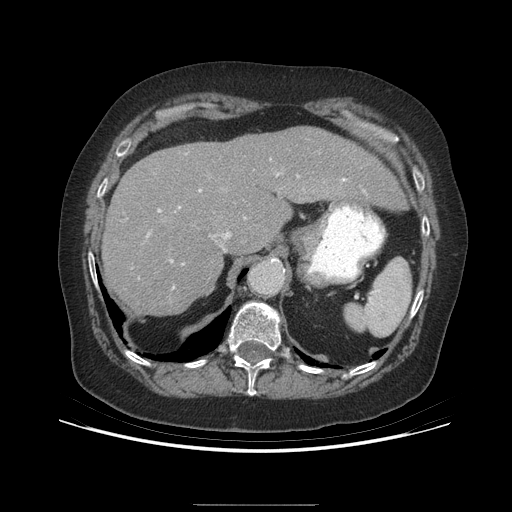
Contrast-enhanced abdominal CT (liver protocol), one axial slice. Reconstruction kernel STANDARD. 140 kVp. Soft-tissue window (W 400 / L 40 HU). 512 × 512 image matrix, field of view 400 × 400 mm. From the clinical record (not read from this slice): diagnosis: hepatocellular carcinoma (patient treated with transarterial chemoembolisation; whether this scan precedes or follows treatment is not stated here); TNM stage (as recorded): Stage-I; Child-Pugh class: A; tumour nodularity: uninodular; tumour size: 3.2 cm.
Structures marked on this image (semi-automatic segmentation, software-assisted and operator-edited):
- liver parenchyma outside the tumour (the mass and vessels are separate outlines, so this box may not span the whole liver): box from (x=102, y=128) to (x=404, y=314) px
- liver vessels: (x=158, y=174)–(x=345, y=289)